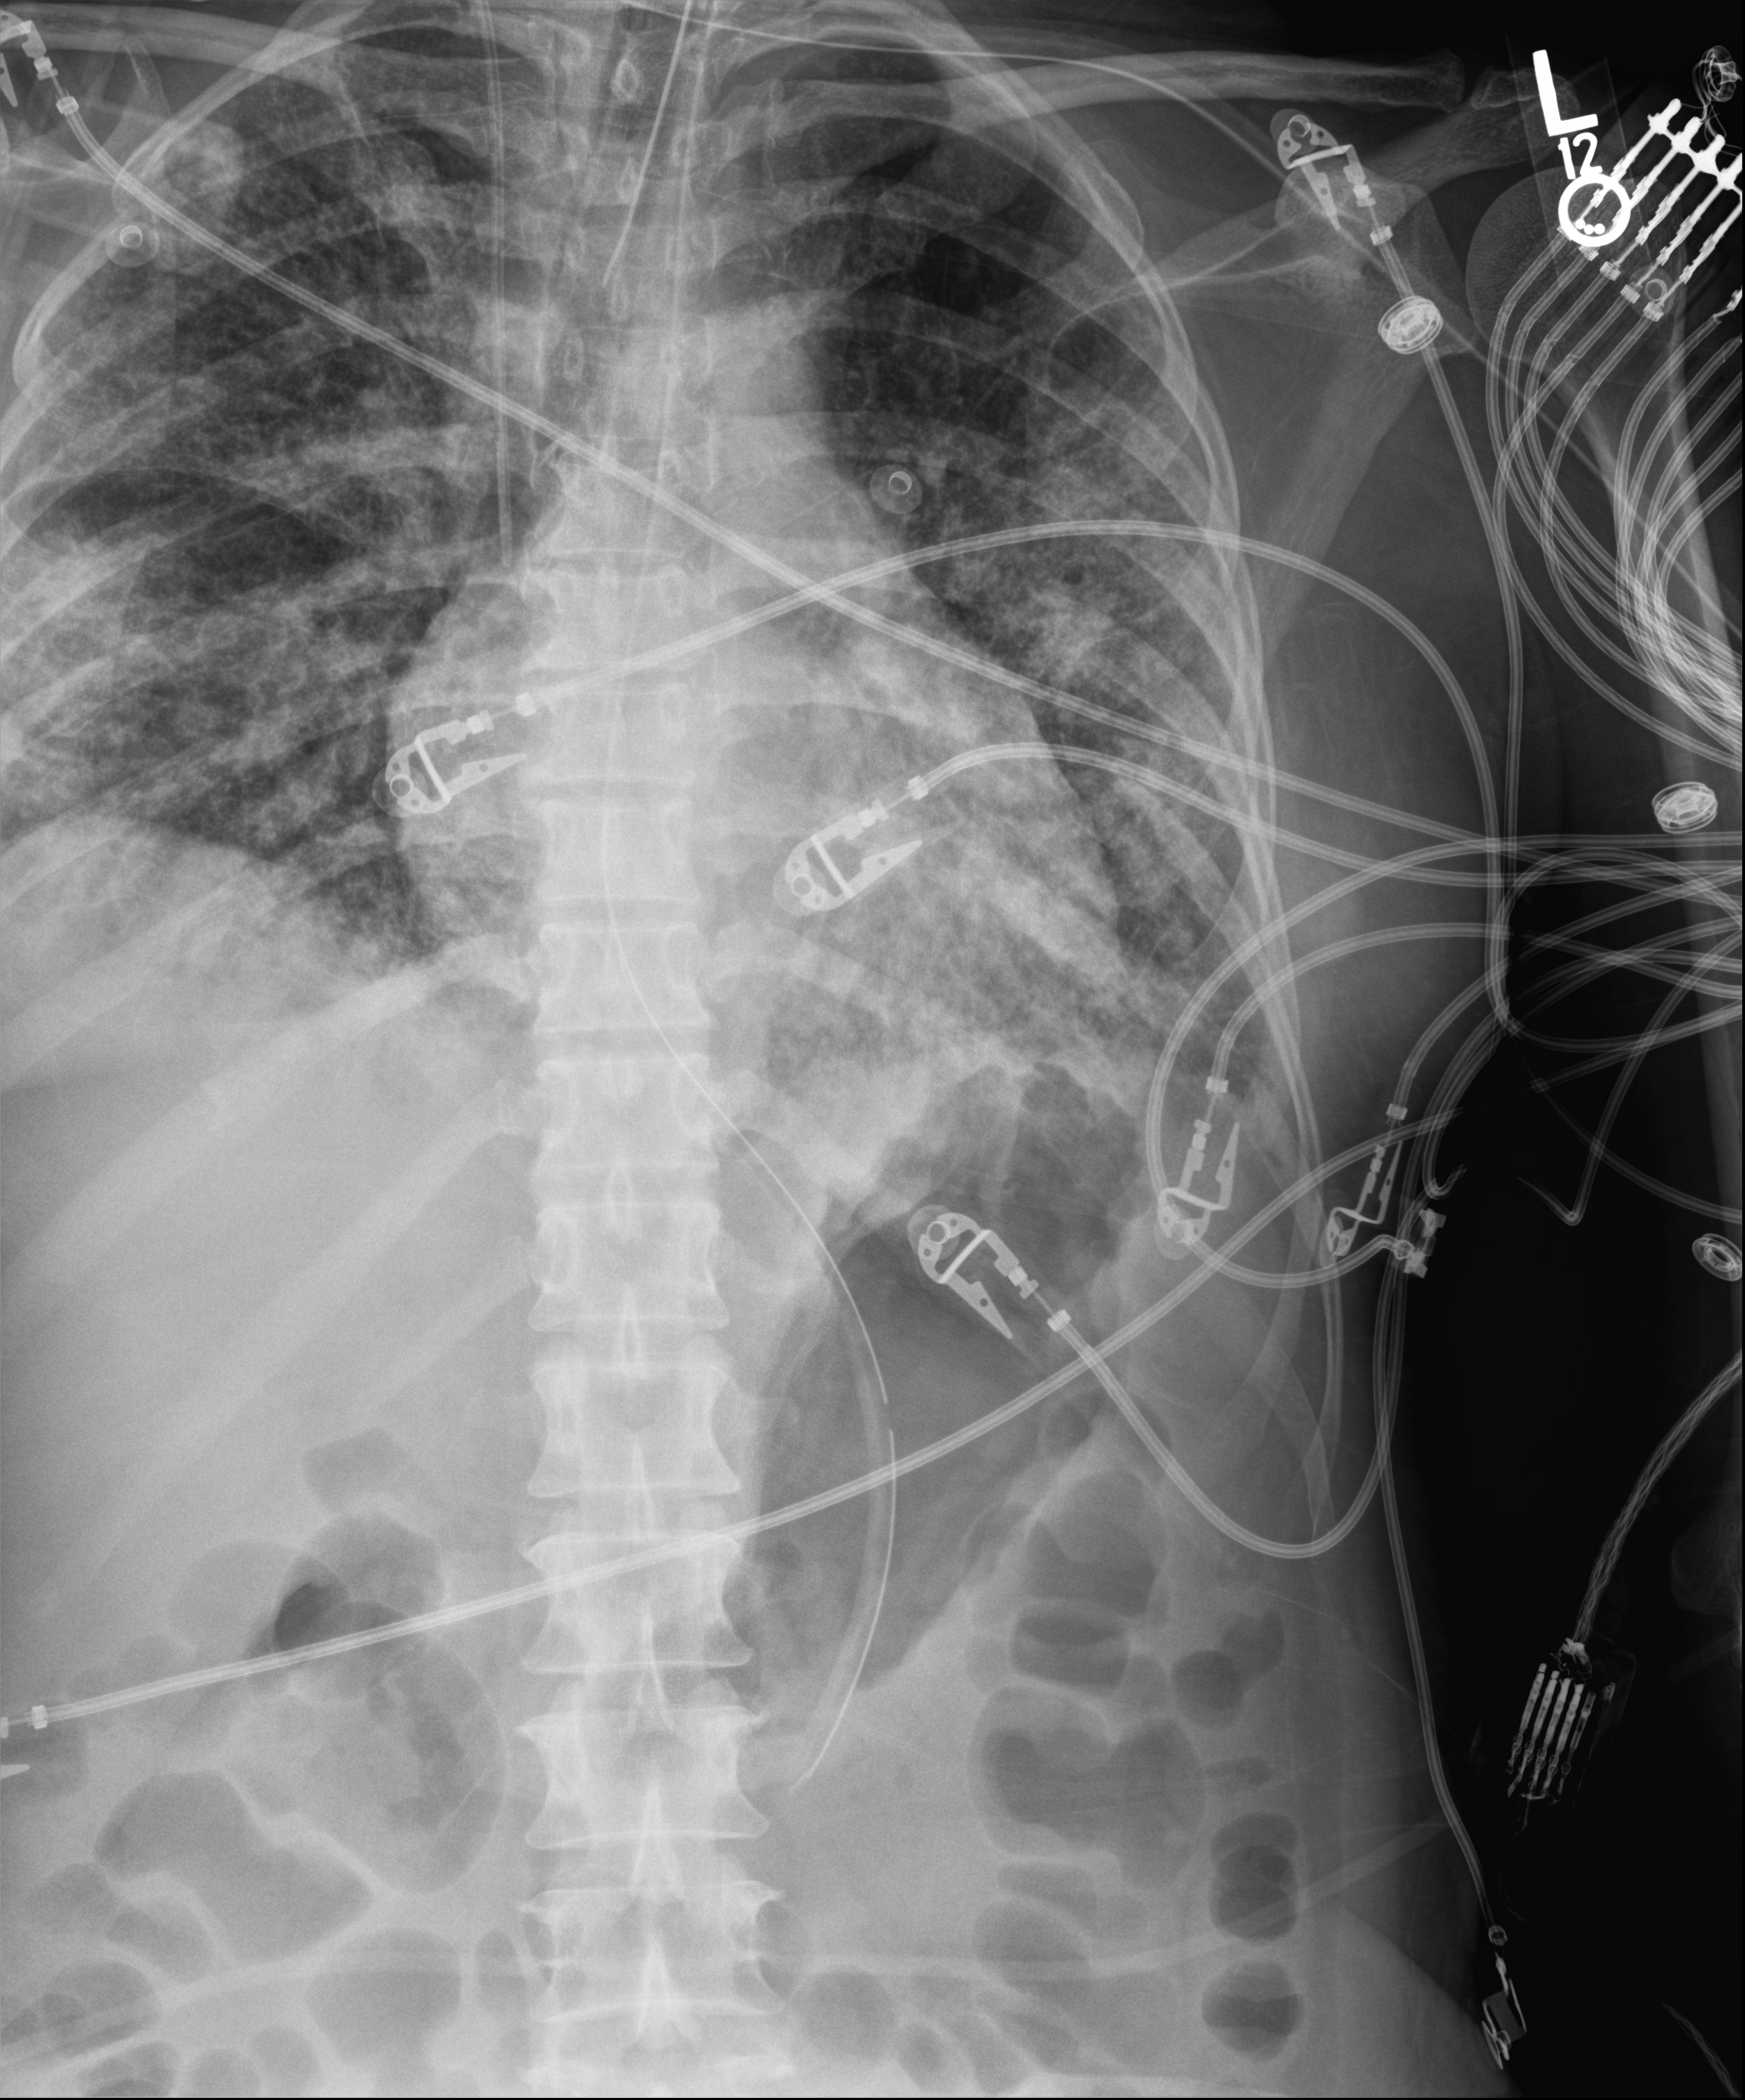
Bedside chest radiograph (digital radiography), anteroposterior (AP) projection. Patient hospitalised with COVID-19; female, aged 18–59 years.
Hospital-stay facts (about this admission, not read from this image; timing relative to this image not recorded): mechanically ventilated during this hospital stay: yes.